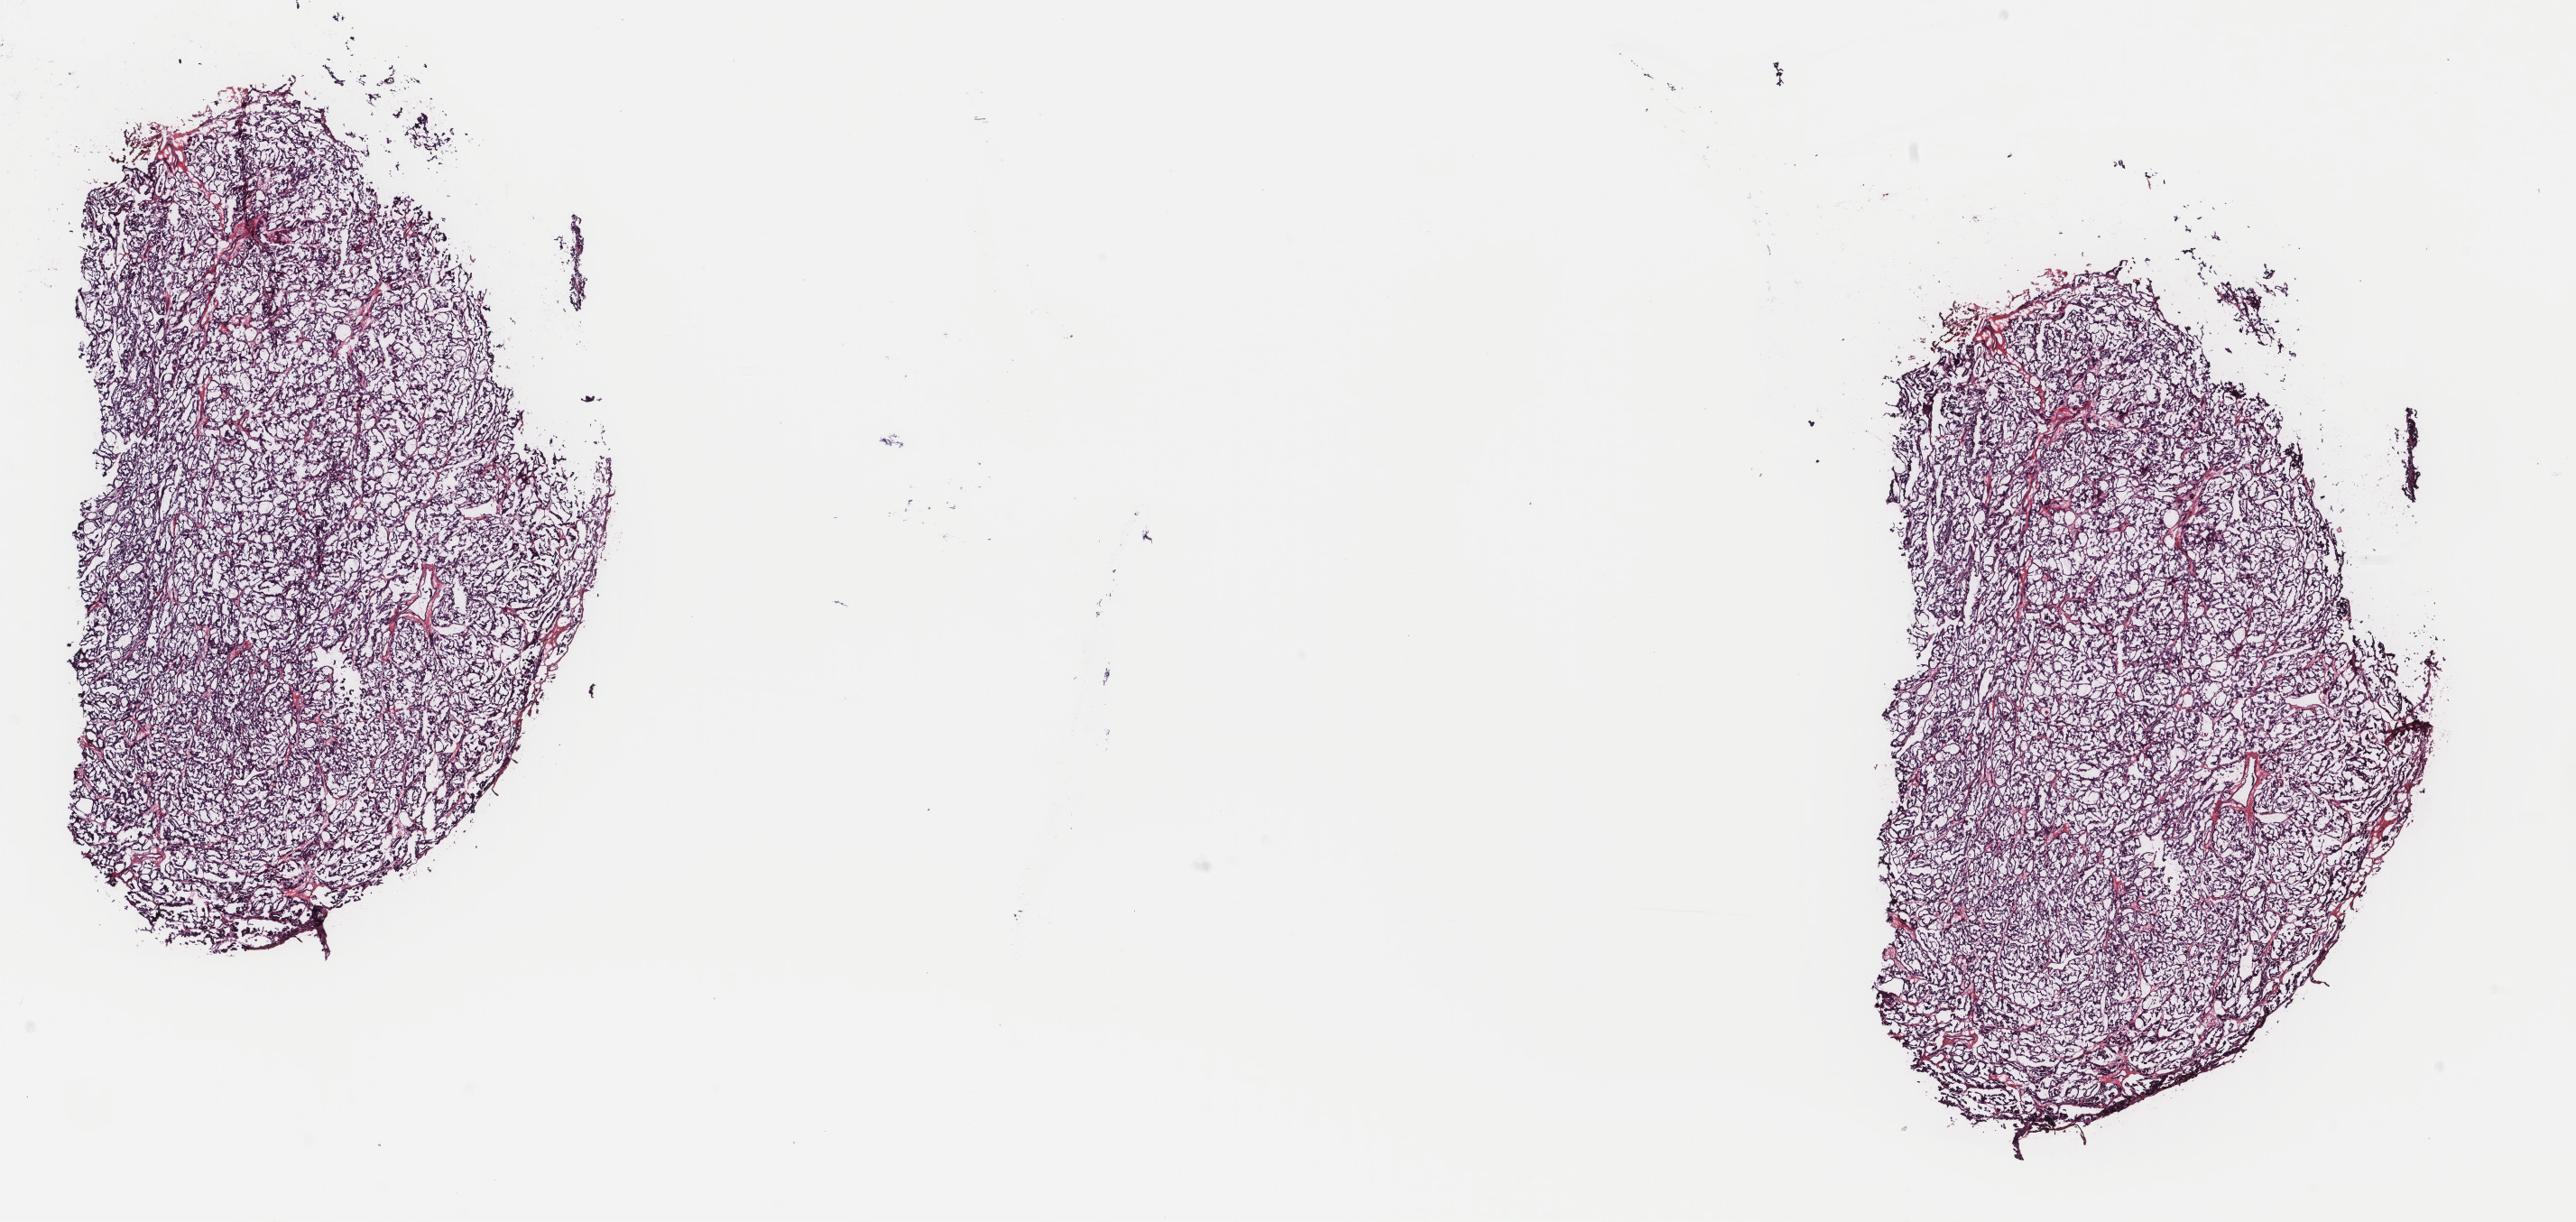
Whole-slide histology image, Hematoxylin and eosin (H&E) stained — a low-resolution overview of the entire scanned area, about 22.7 x 10.7 mm. Frozen section from the top of the tissue portion. Primary tumour sample from the thyroid. Patient: female, age at initial diagnosis 23 years. Pathologist review of this section (percent, as recorded): tumour cells 100%, tumour nuclei 80%, normal cells 0%, stromal cells 0%, necrosis 0%. Inflammatory infiltration, as recorded: lymphocyte infiltration 2%, monocyte infiltration 0%, neutrophil infiltration 0%.
- lymph nodes positive (case pathology): 0 of 3 examined
- AJCC pathologic stage: I (7th edition)
- pathologic diagnosis: Papillary adenocarcinoma, NOS (thyroid gland)